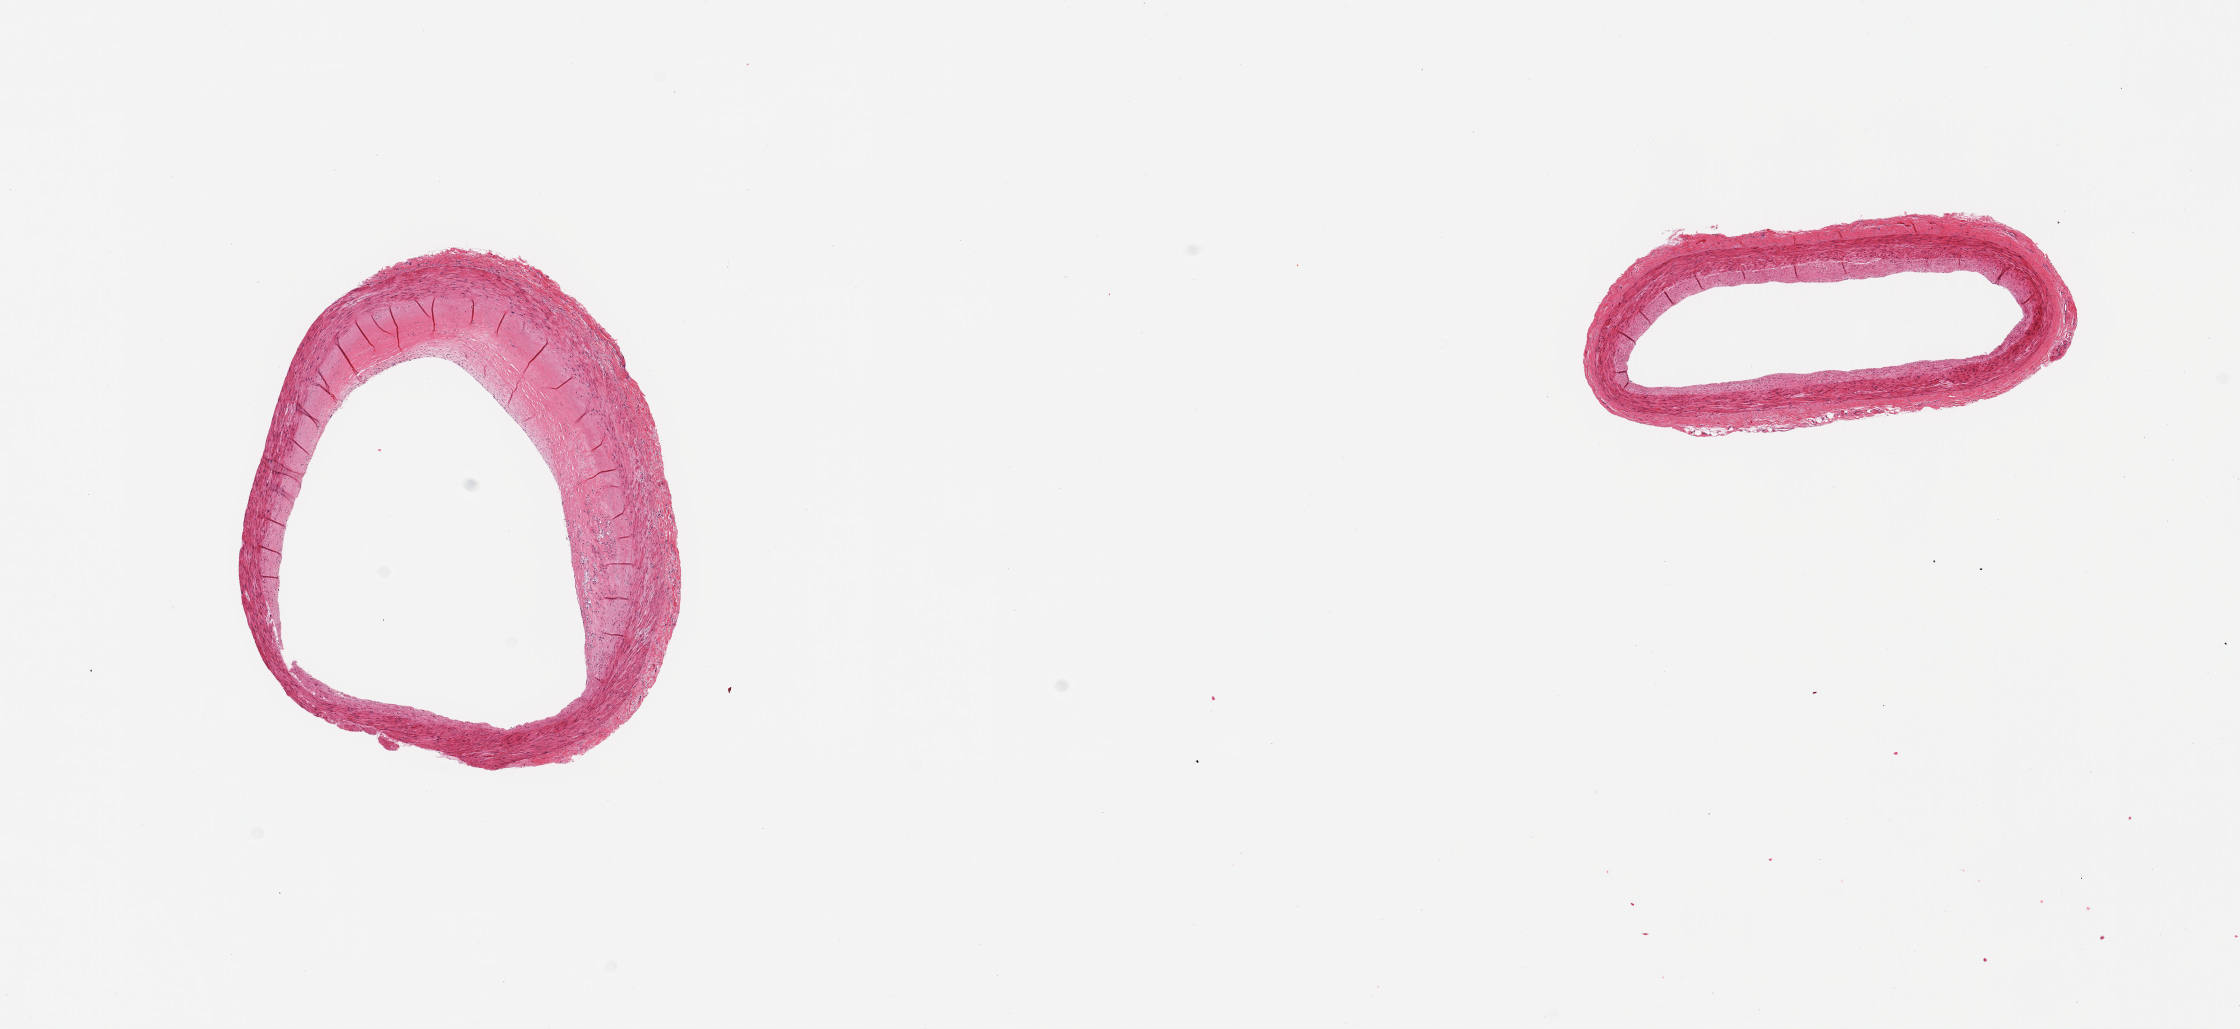
H&E whole-slide image, low-resolution overview of the scanned area, about 17.7 x 8.1 mm. PAXgene-fixed, paraffin-embedded tissue. Target tissue: coronary artery. Tissue donor sample. Donor sex: female.
Reviewer comment on this tissue sample: 2 pieces; mild eccentric fibrotic plaques up to 0.6 mm.